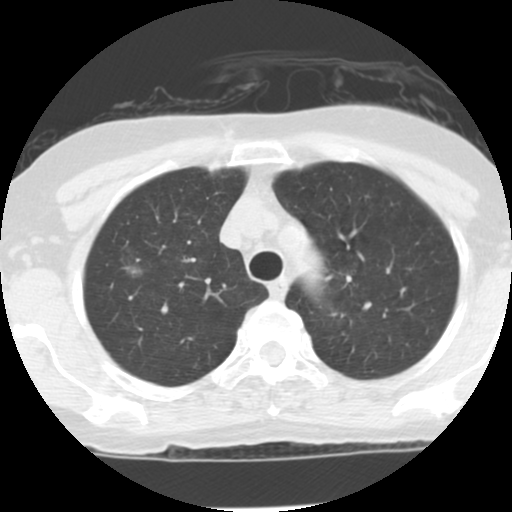
Low-dose screening chest CT, one axial slice. Slice 98 of 122 in the series (ordered by position). 120 kVp. Lung window (W 1500 / L -600 HU). 2.5 mm slice thickness. 512 × 512 image matrix, field of view 290 × 290 mm.
Annotated regions visible in this slice (outlined manually by an expert reader):
- lesion 1 (tumor, upper lobe of right lung): bounding box [x1, y1, x2, y2] px = [128, 264, 144, 278]